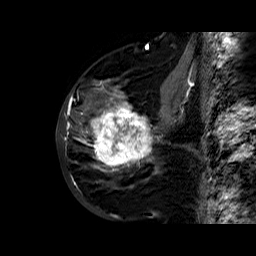
Breast MRI (dynamic contrast-enhanced), one sagittal slice. Position 24 of 60 along the scan axis. Dynamic contrast-enhanced series, time point 2 of 6 at this slice position (early post-contrast). 1.5 T. TE 6.4 ms, TR 32.8 ms. 4 mm slice thickness. 256 × 256 image matrix, field of view 200 × 200 mm. Female patient. Case-level facts recorded for this patient, not image findings: setting: breast cancer imaged before/during neoadjuvant chemotherapy; receptor status: HR-positive, HER2-negative.
Annotated regions visible in this slice (semi-automatically segmented with operator editing):
- analysis volume of interest (the breast-tissue region the enhancement analysis was run in; not a lesion): bounding box [x1, y1, x2, y2] px = [86, 78, 163, 177]
- tumour enhancement mask (voxels above the 100 % enhancement threshold inside the analysis volume of interest): [90, 79, 153, 172]